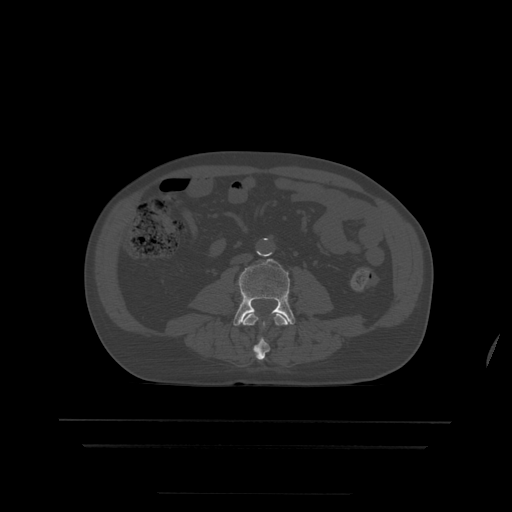
CT including the spine, one axial slice. Position 104 of 522 along the scan axis. Bone window (W 1800 / L 400 HU). 1.25 mm slice thickness. 512 × 512 image matrix, field of view 436 × 436 mm. Patient age 68 years. Case-level facts recorded for this patient, not image findings: primary cancer: urothelial.
Structures marked on this image (semi-automatic segmentation, software-assisted and operator-edited):
- L3 vertebra: bounding box [x1, y1, x2, y2] px = [241, 313, 292, 360]
- L4 vertebra: [233, 259, 296, 327]